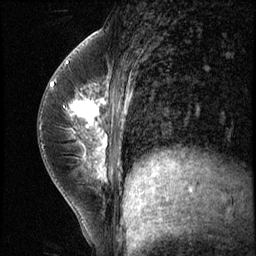
Breast MRI (dynamic contrast-enhanced), one sagittal slice; slice 25 of 56 in the series (ordered by position); 3 images stored at this slice position (order not interpretable as contrast timing); 1.5 T; TE 4.2 ms, TR 8.7 ms; 2.5 mm slice thickness; 256 × 256 image matrix, field of view 180 × 180 mm. Female patient, age 35 years. From the clinical record (not read from this slice): setting: breast cancer imaged before/during neoadjuvant chemotherapy; receptor status: HER2-positive.
Annotated regions visible in this slice (semi-automatic segmentation, software-assisted and operator-edited):
- analysis volume of interest (the breast-tissue region the enhancement analysis was run in; not a lesion): bounding box <58,84,138,186> (left, top, right, bottom; pixels)
- tumour enhancement mask (voxels above the 140 % enhancement threshold inside the analysis volume of interest): <63,91,126,181>